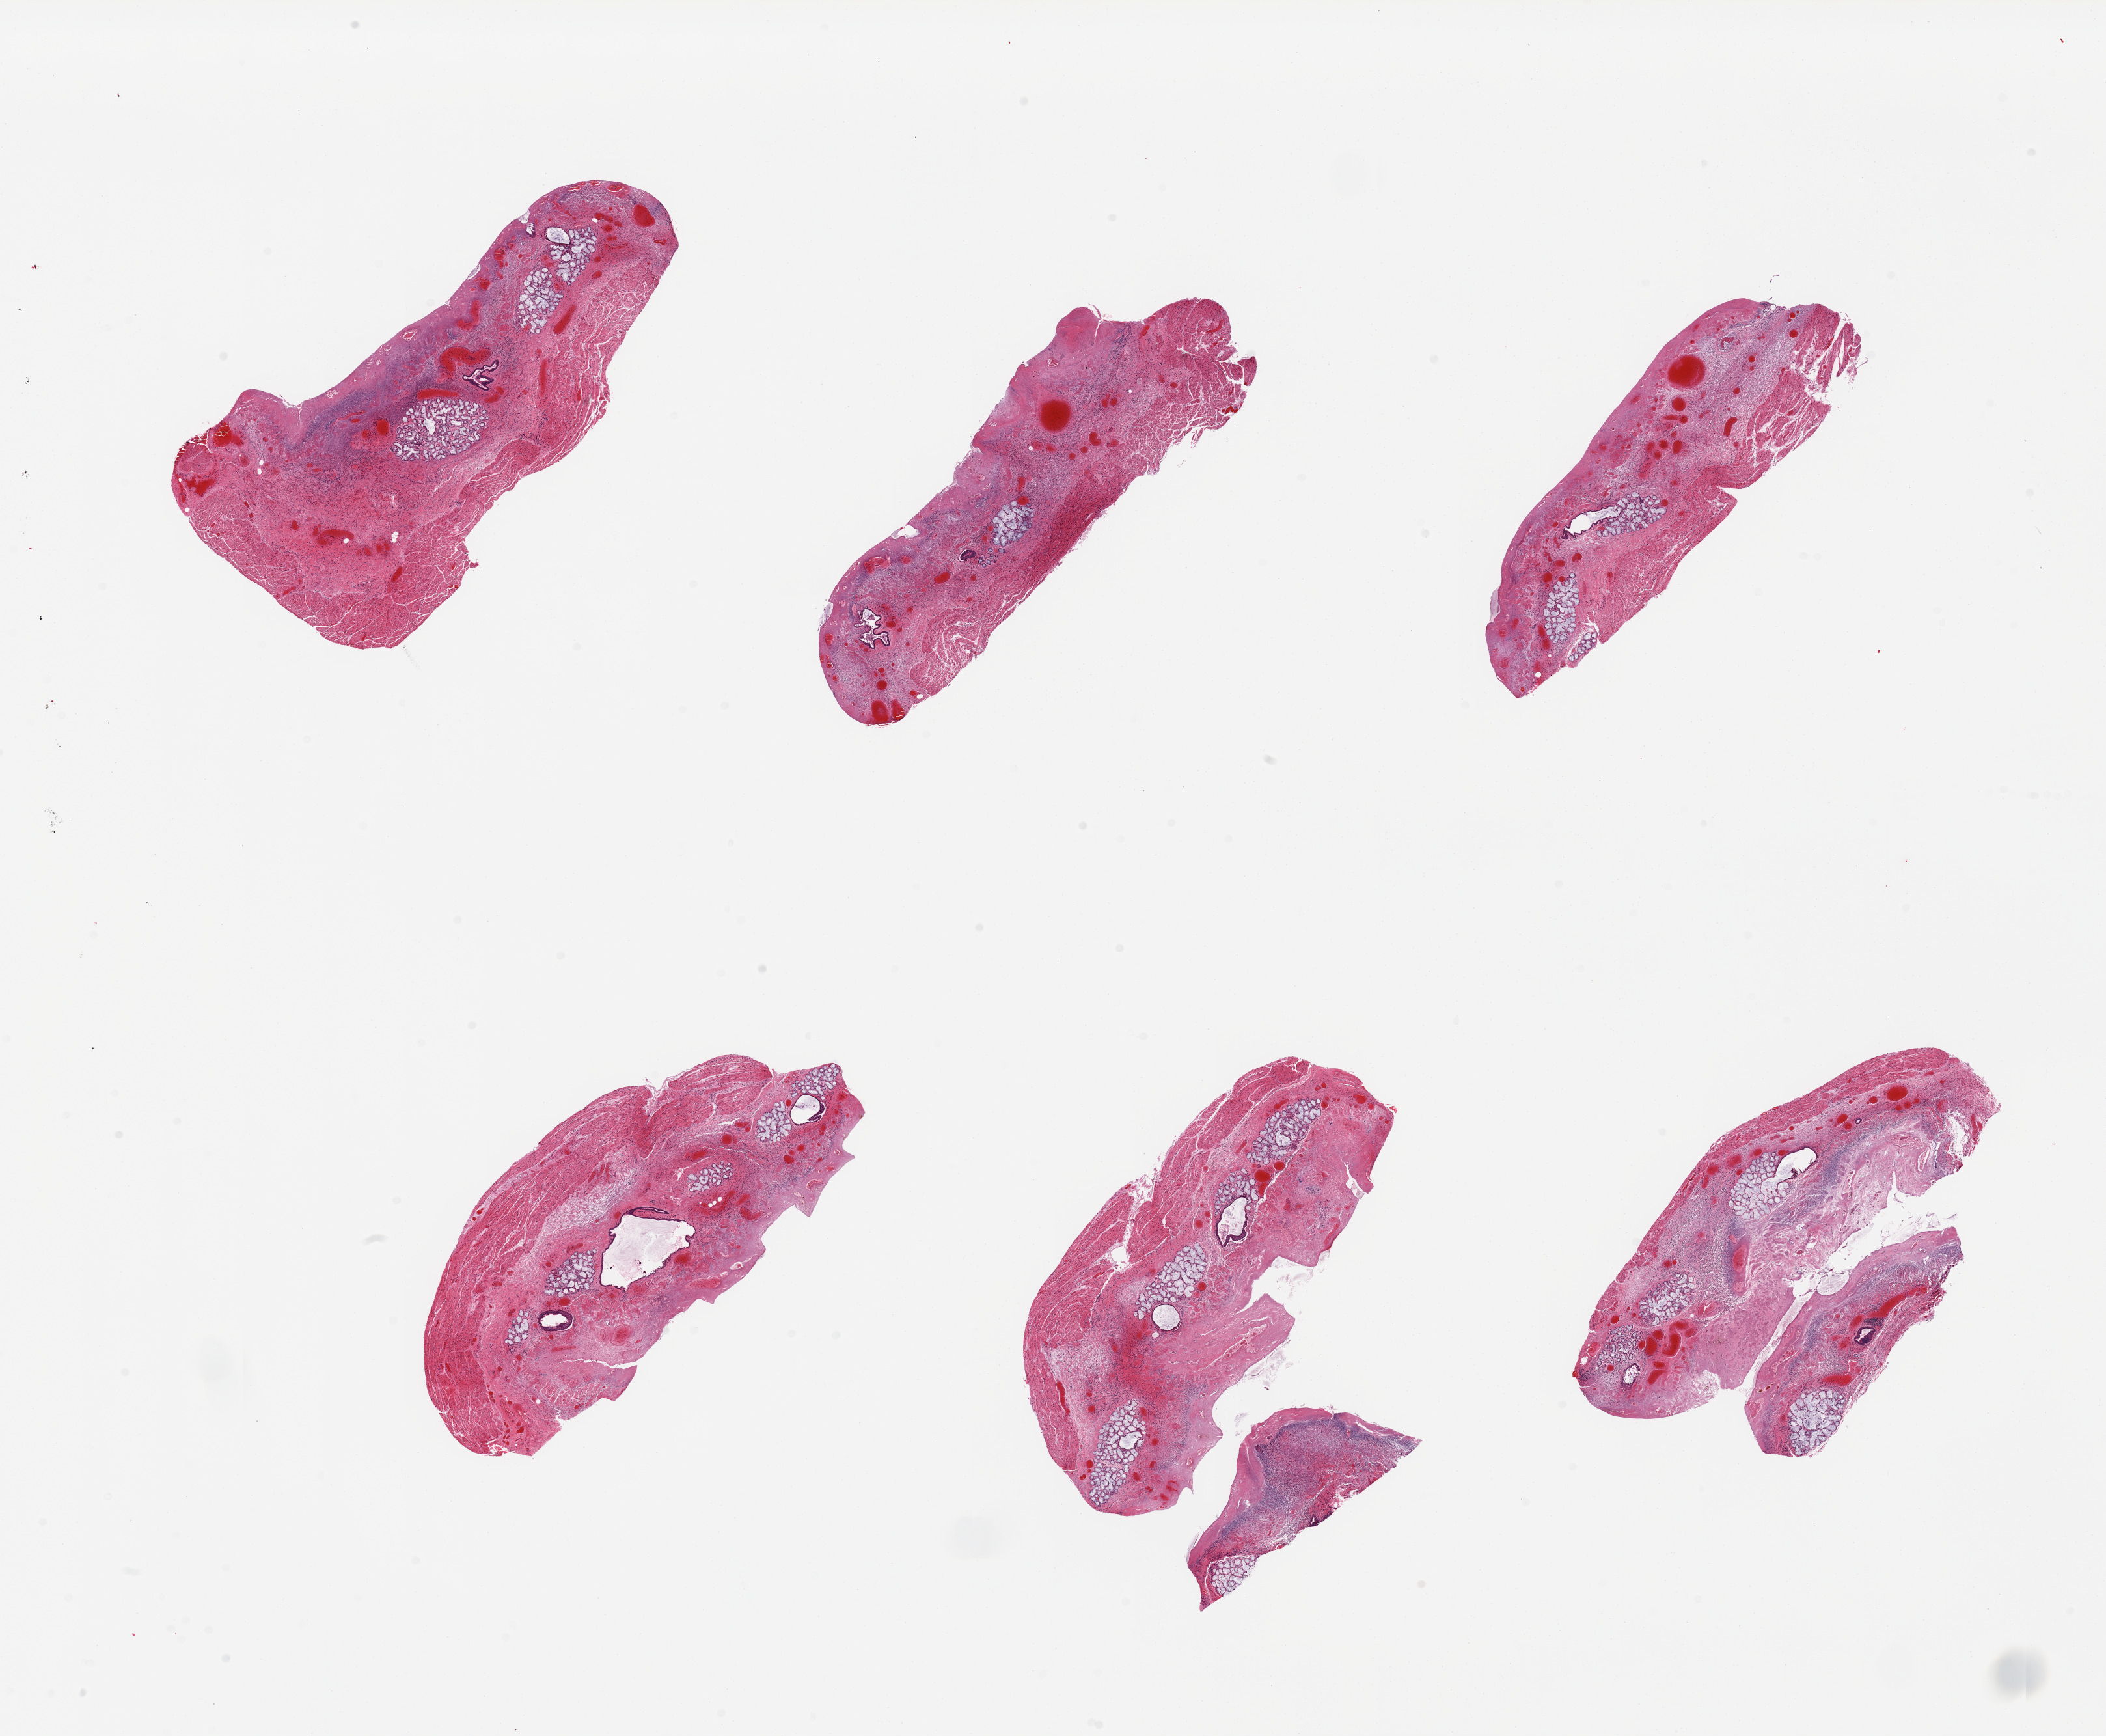
Digitized haematoxylin and eosin-stained section, a low-resolution overview of the entire scanned area, about 25.6 x 21.1 mm (from a 20x scan); PAXgene-fixed, paraffin-embedded tissue; section of esophageal mucous membrane (target tissue); tissue donor sample.
• review note (as recorded): 6 pieces, badly autolyzed, no mucosa